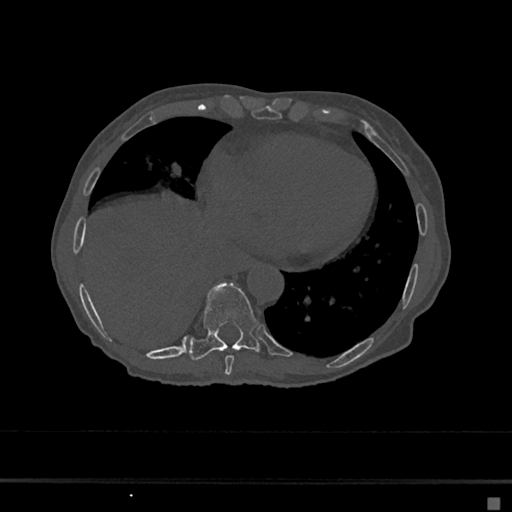
CT including the spine, one axial slice. Position 282 of 797 along the scan axis. Reconstruction kernel Br40s/3. Bone window (W 1800 / L 400 HU). 512 × 512 image matrix, field of view 360 × 360 mm. Female patient, age 68 years. From the clinical record (not read from this slice): primary cancer: renal.
Annotated regions visible in this slice (semi-automatically segmented with operator editing):
- T8 vertebra: bounding box <225,355,235,375> (left, top, right, bottom; pixels)
- T9 vertebra: <189,283,260,360>